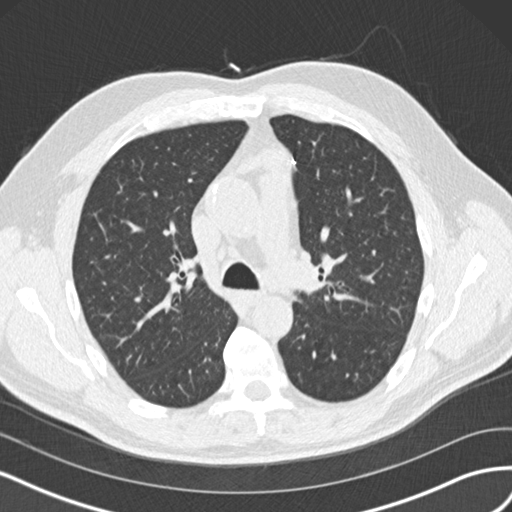
Axial slice from a low-dose chest CT screening exam. First (baseline) screen. Lung window (W 1500 / L -600 HU). Standard (soft-tissue) reconstruction kernel (B30f). Slice 55 of 160 in the series. Male participant, aged 65 years at enrolment.
Expert reader's lesion annotation, bounding box <307,242,353,296> (left, top, right, bottom; pixels). The screening reader recorded 4 non-calcified nodules or masses ≥4 mm on this exam (left upper lobe, left upper lobe, right upper lobe, right middle lobe); which of them this box marks is not recorded.